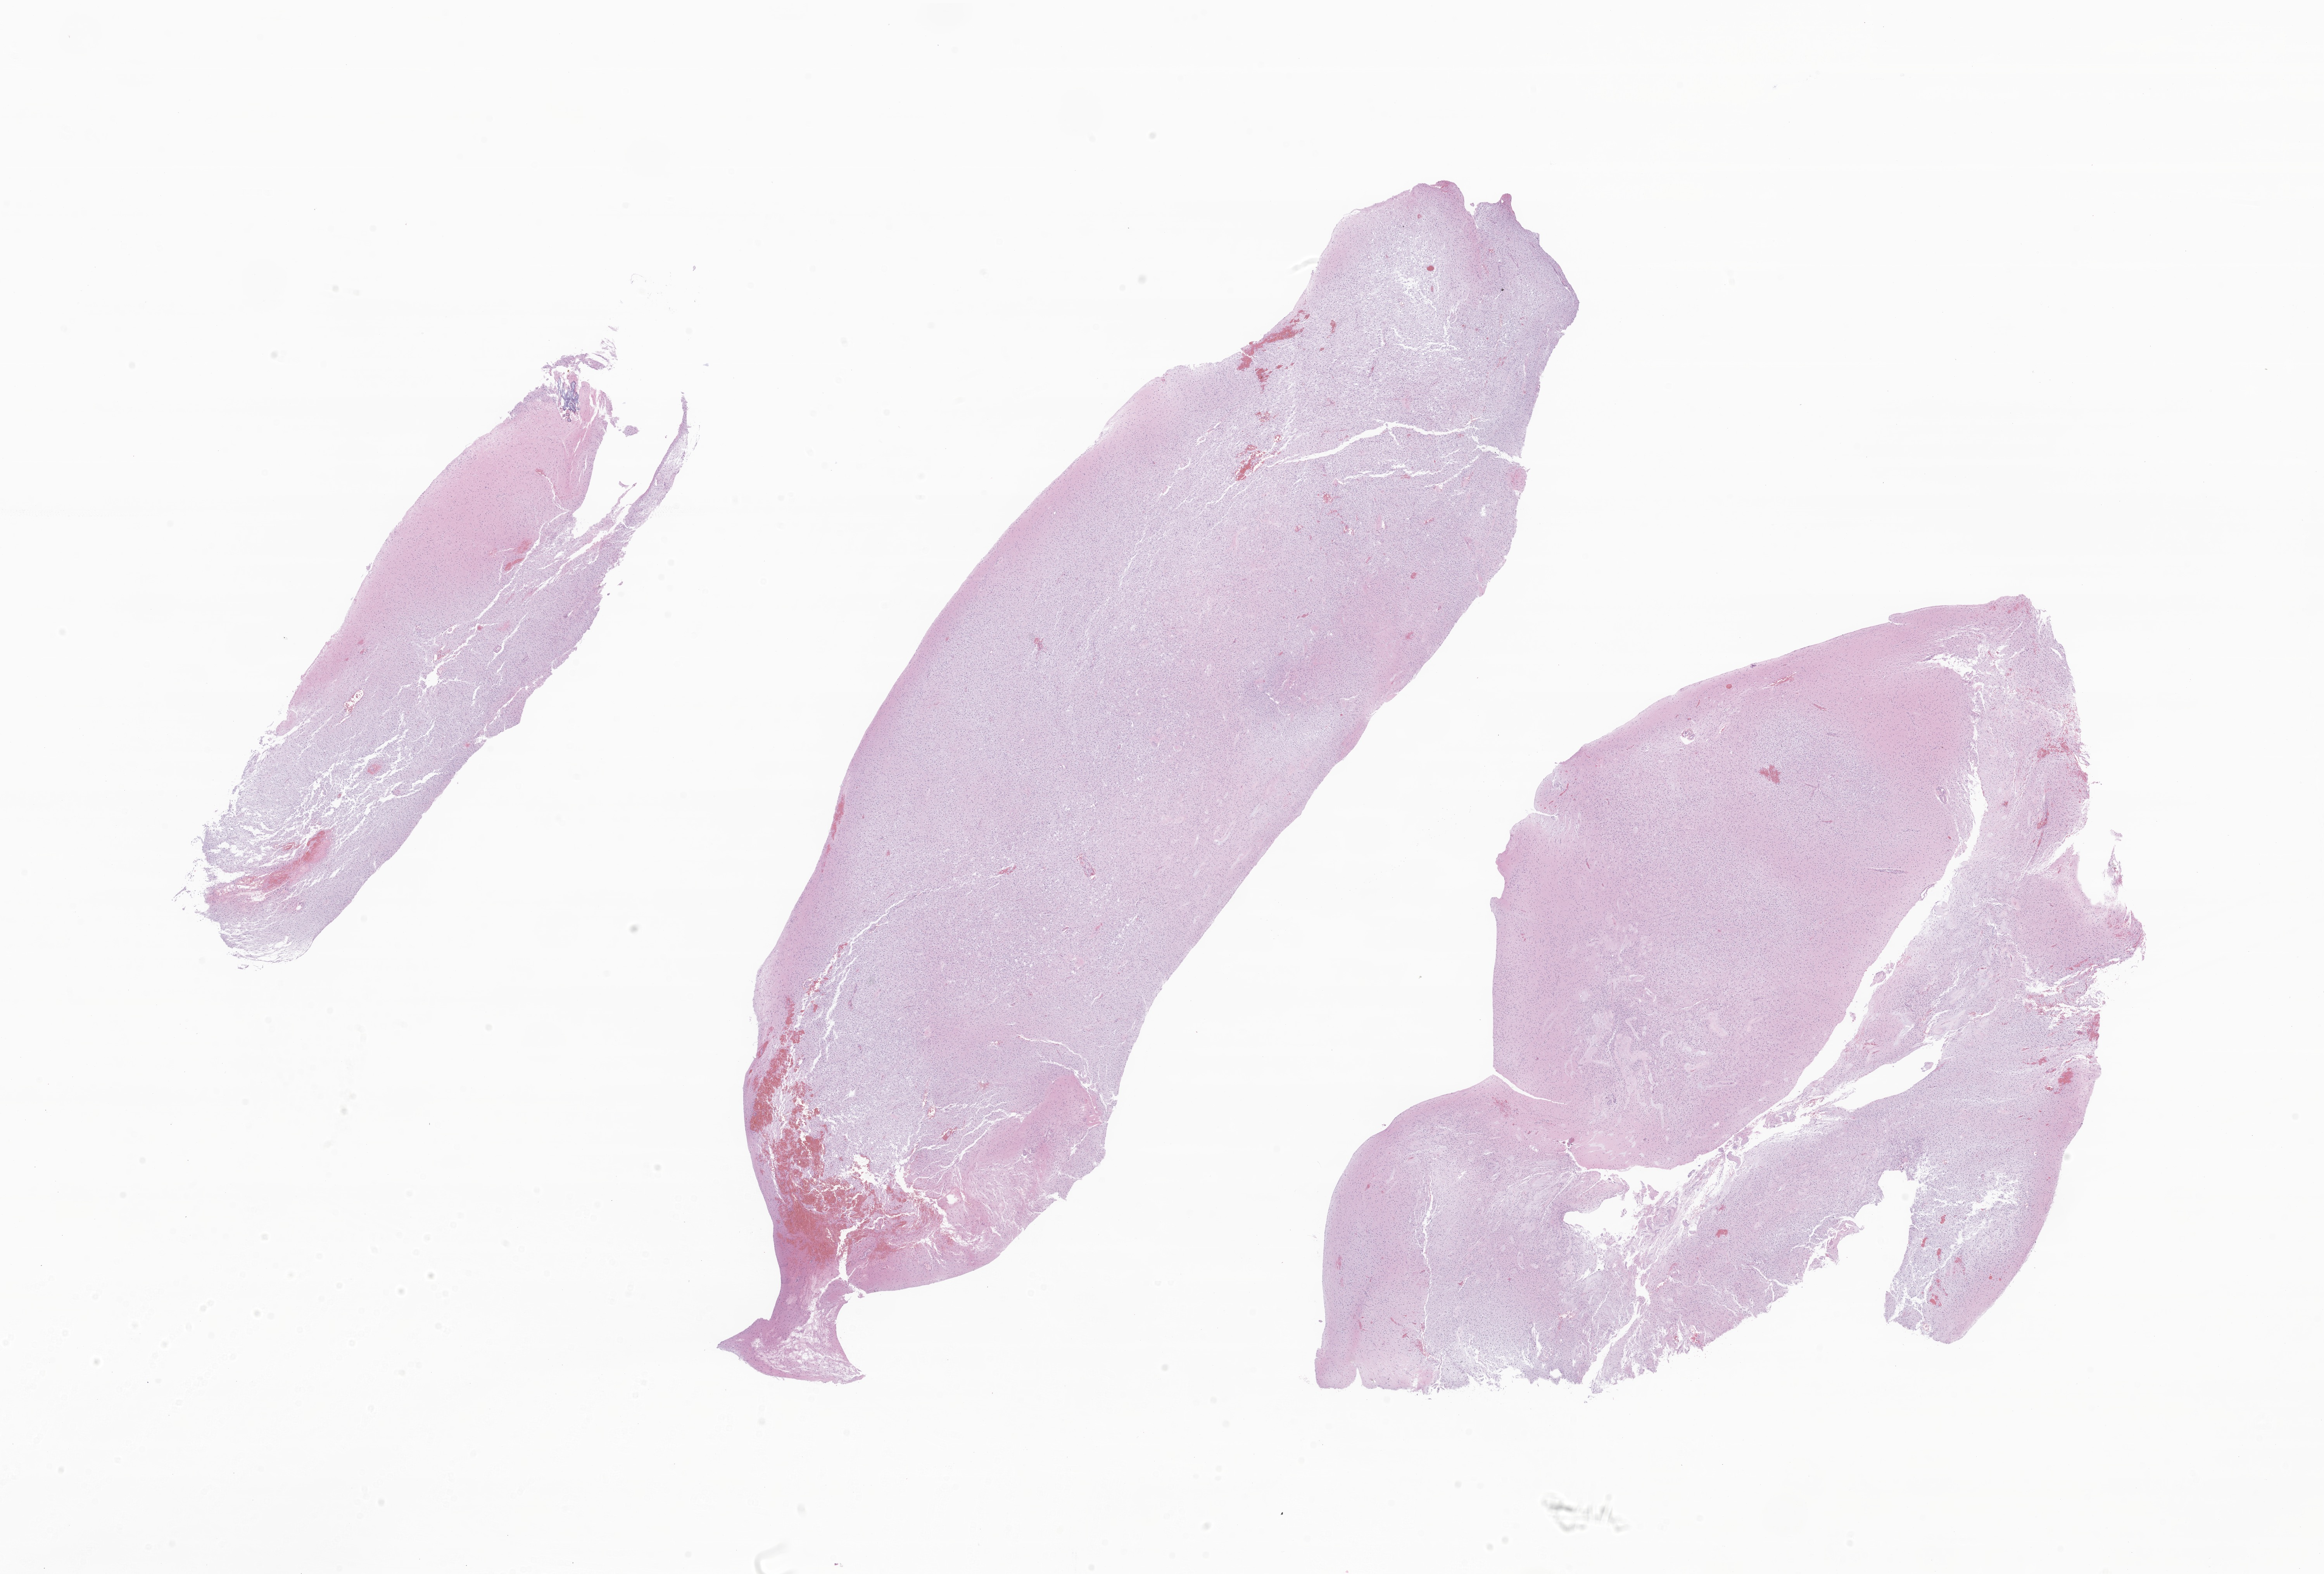
Whole-slide image, haematoxylin and eosin stain of tumor tissue from the brain, low-resolution overview of the scanned area, about 25.3 x 17.1 mm; FFPE section. Patient male; age 148 months (12 years 4 months).
• diagnosis (ICD-O-3 morphology term): Astrocytoma, NOS